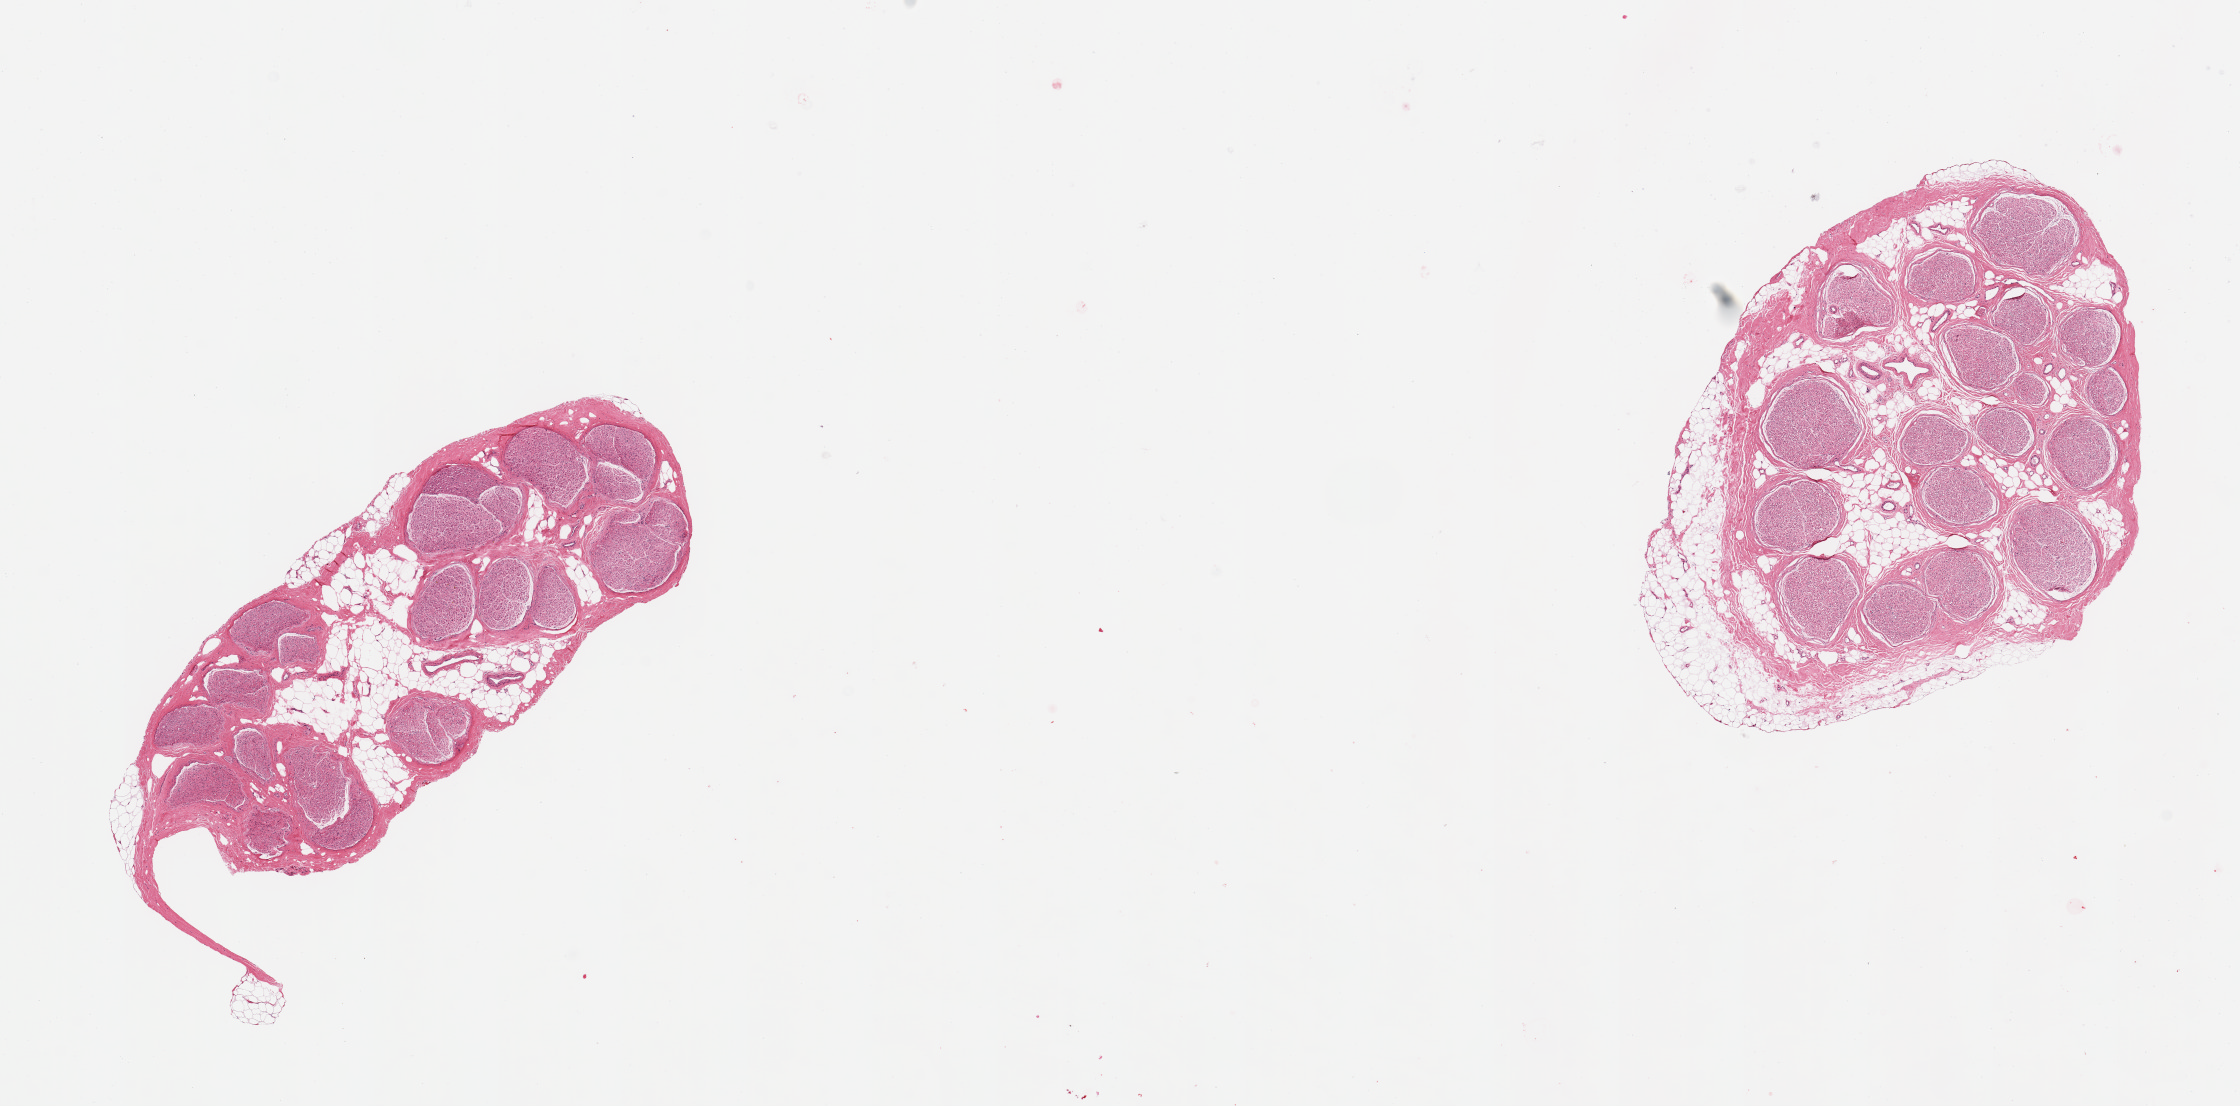
Digitized H&E-stained section — low-resolution overview of the scanned area, about 17.7 x 8.7 mm, PAXgene-fixed, paraffin-embedded tissue, section of tibial nerve (target tissue), tissue donor sample. Donor sex: male.
• review note (as recorded): 2 pieces; 20% internal and external fat content